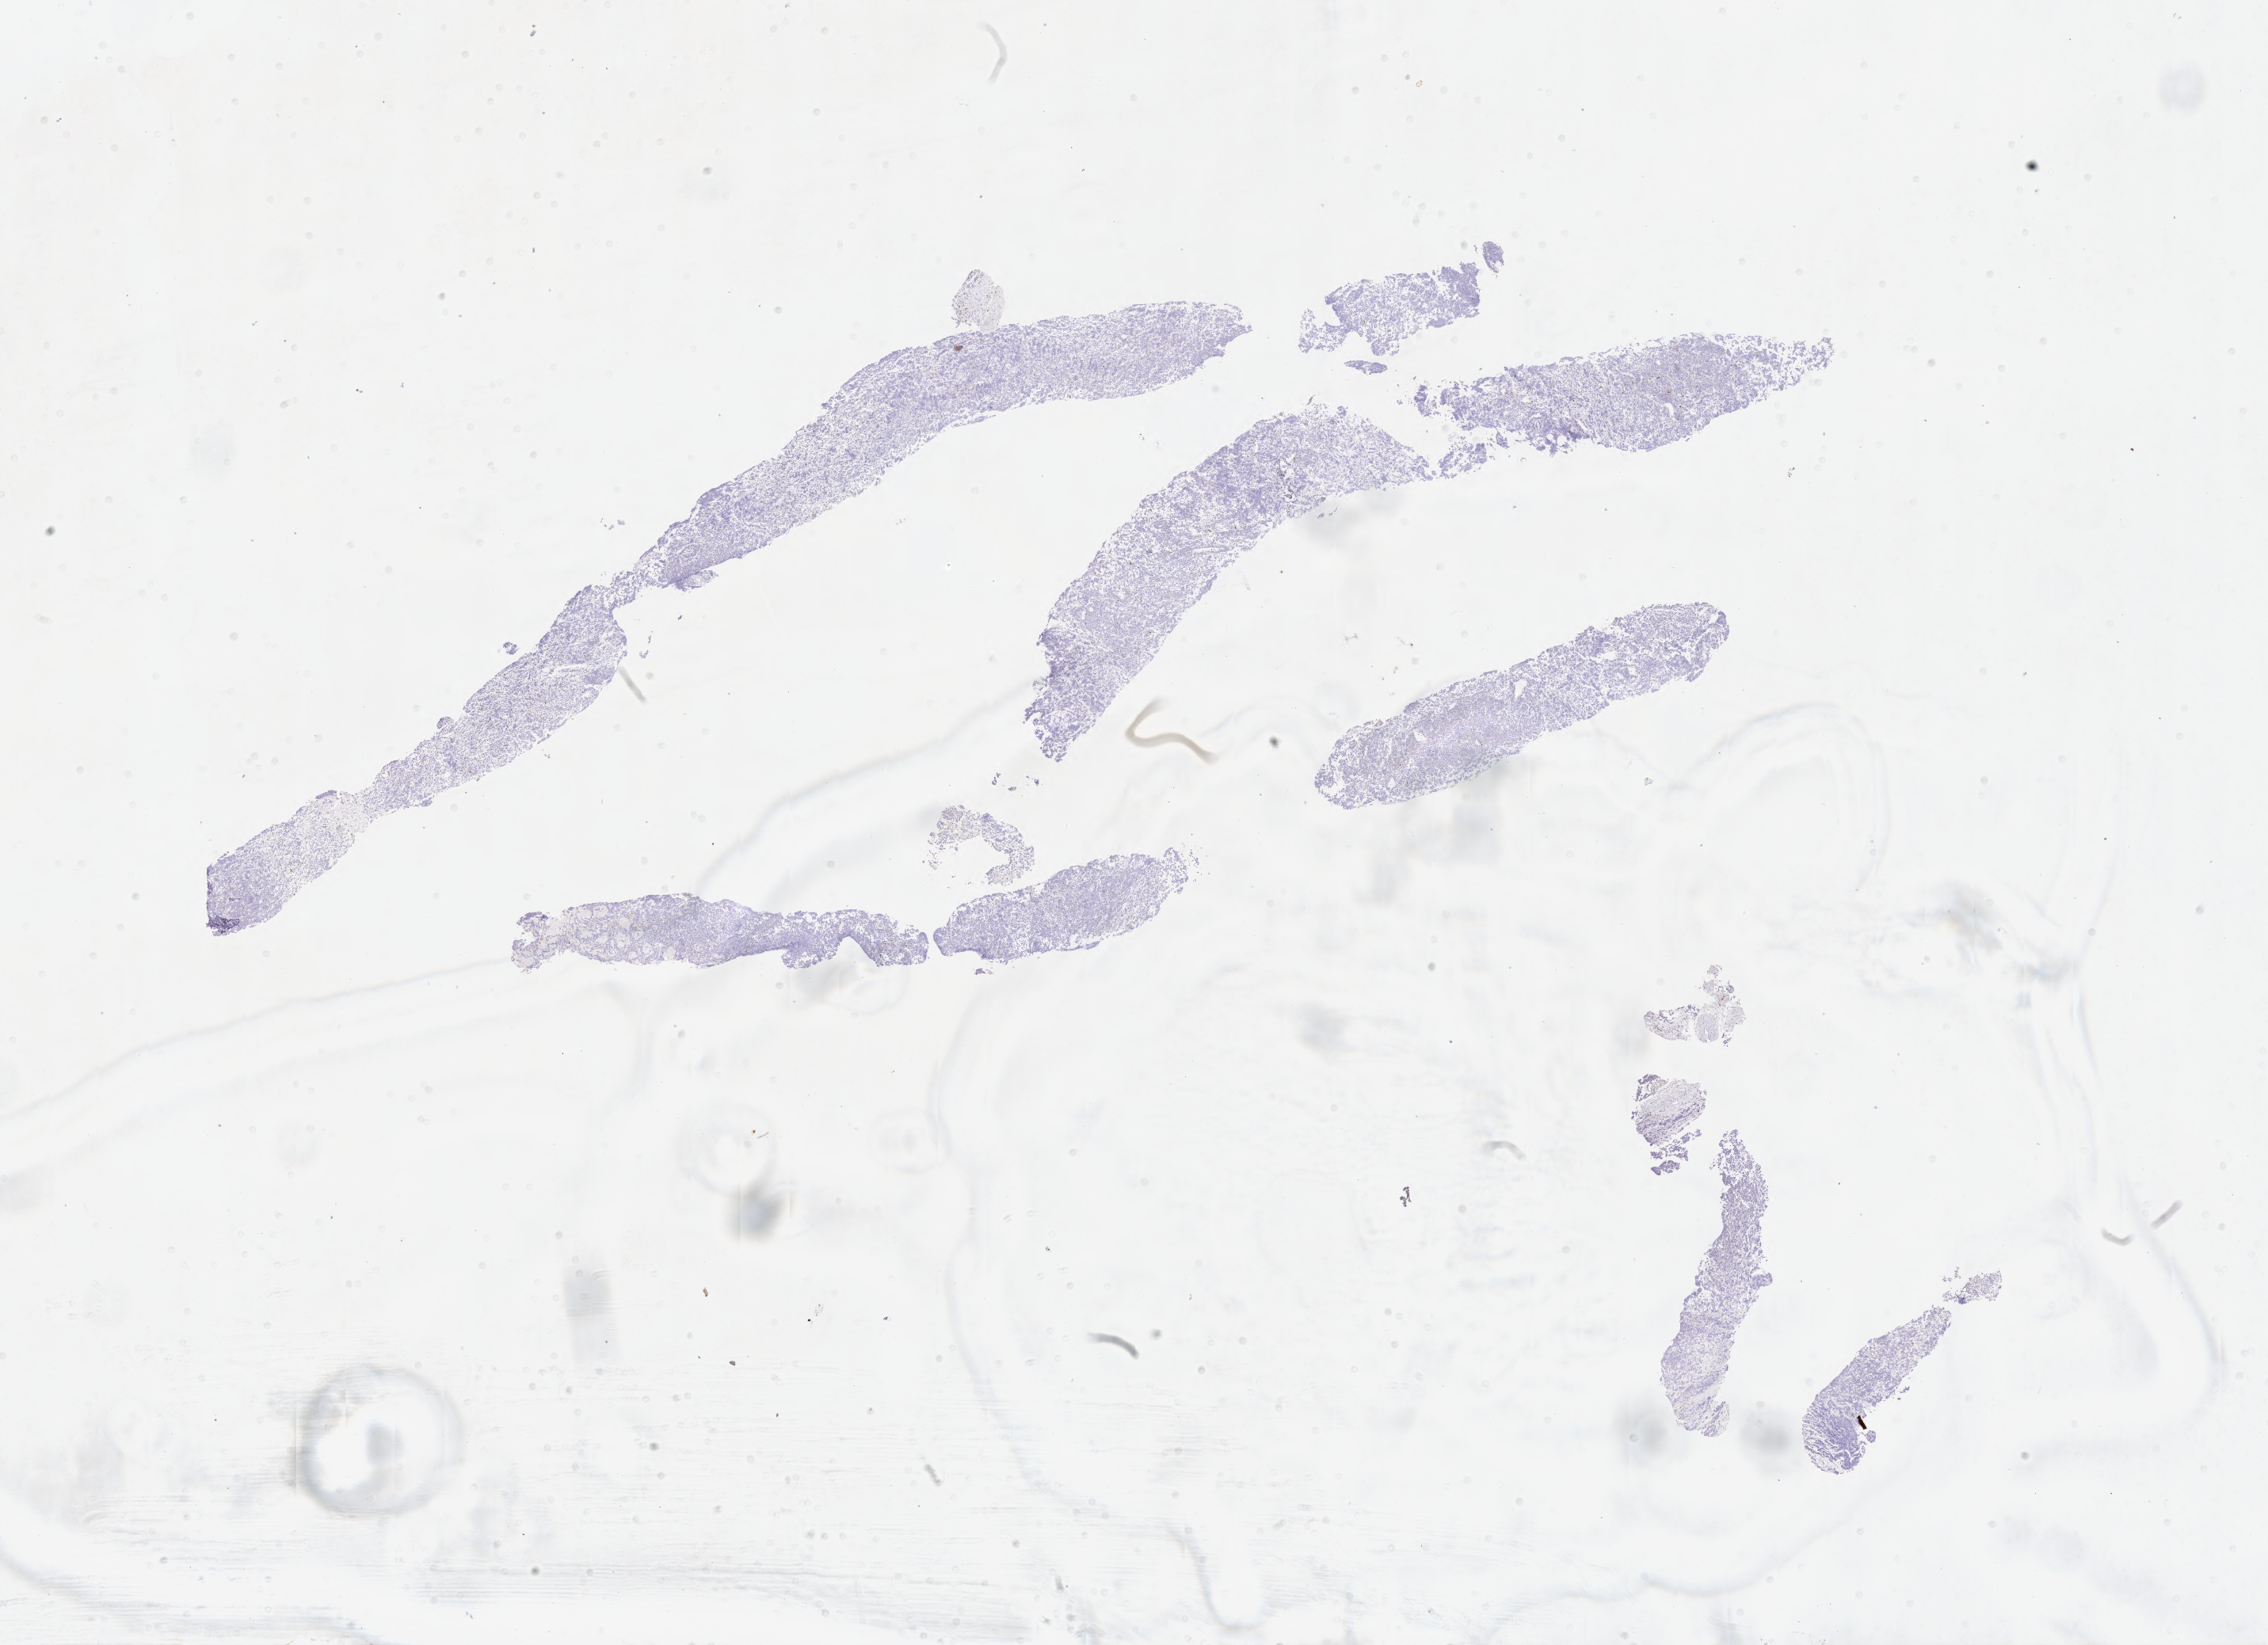
Immunohistochemistry (IHC) whole-slide image stained for CD5, shown as a low-resolution overview of the whole scanned area (about 23.1 x 16.8 mm); specimen: tumor tissue. Male patient, 66 years old.
Histologic diagnosis: Burkitt lymphoma, NOS.